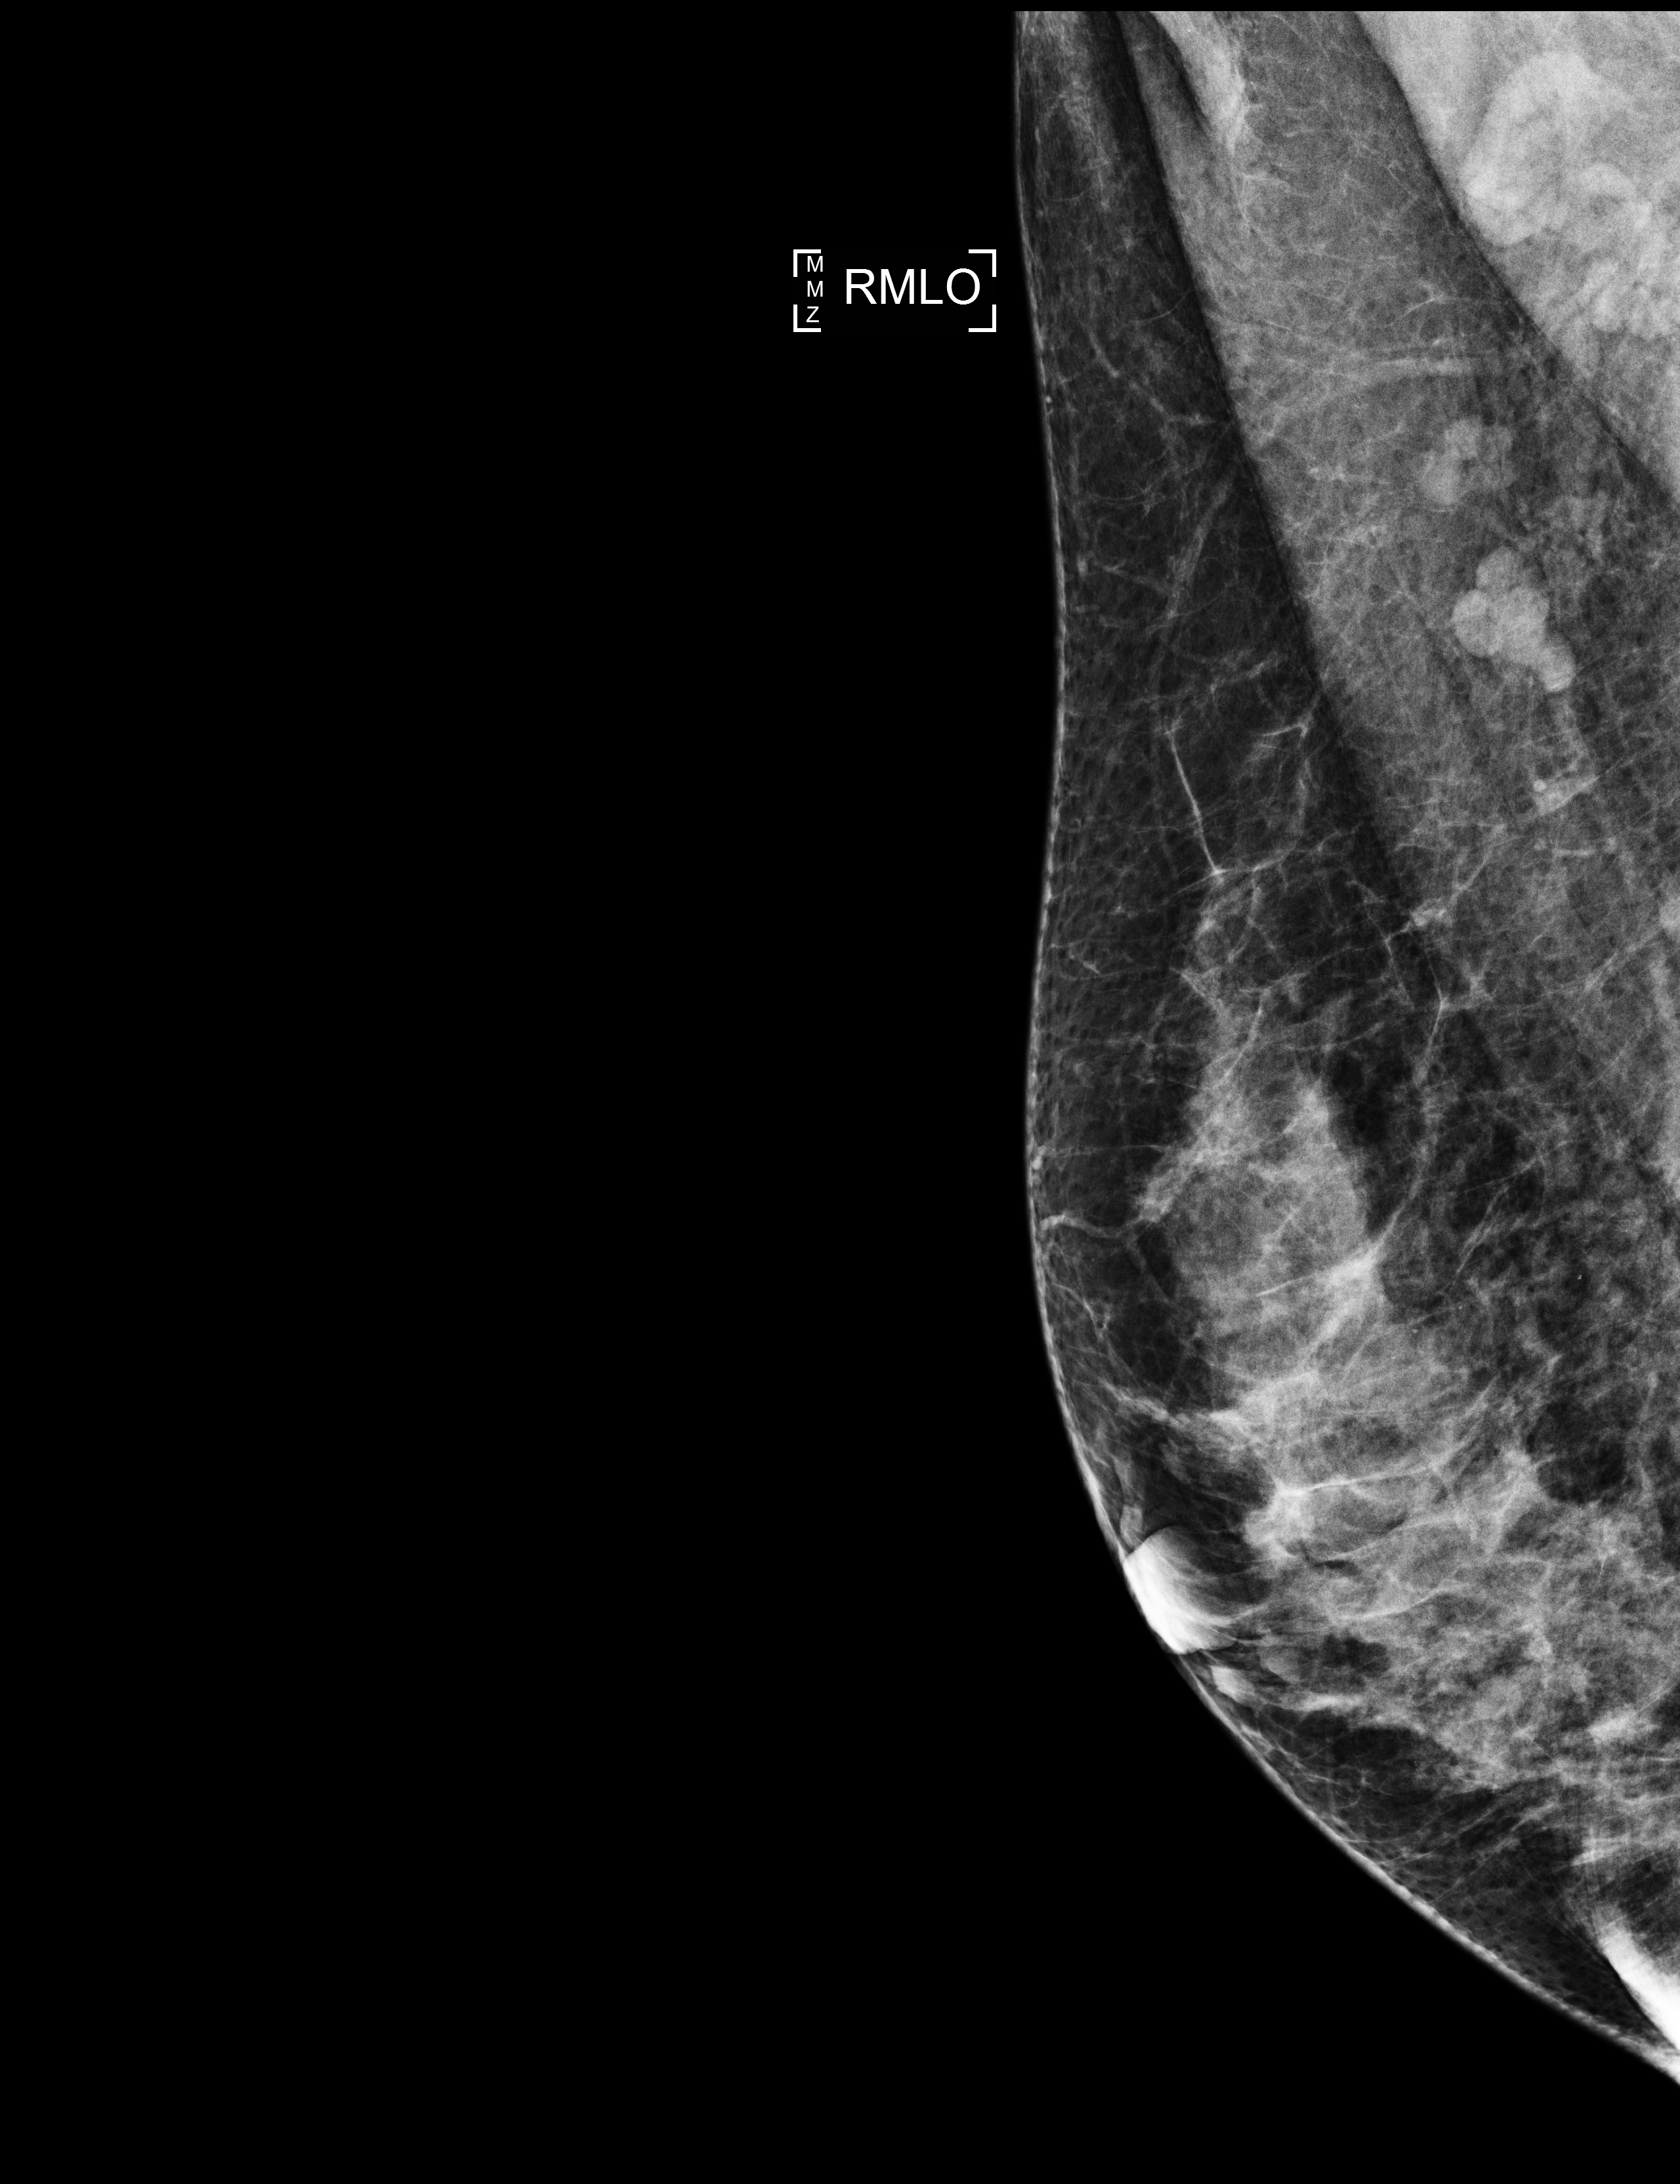
Digital mammogram (FFDM), right breast, medio-lateral oblique projection, annual screening mammography examination, system: Selenia Dimensions. Patient aged 47 years (female).
Final BI-RADS category for the screening round (tomosynthesis exam, both breasts): category 1.